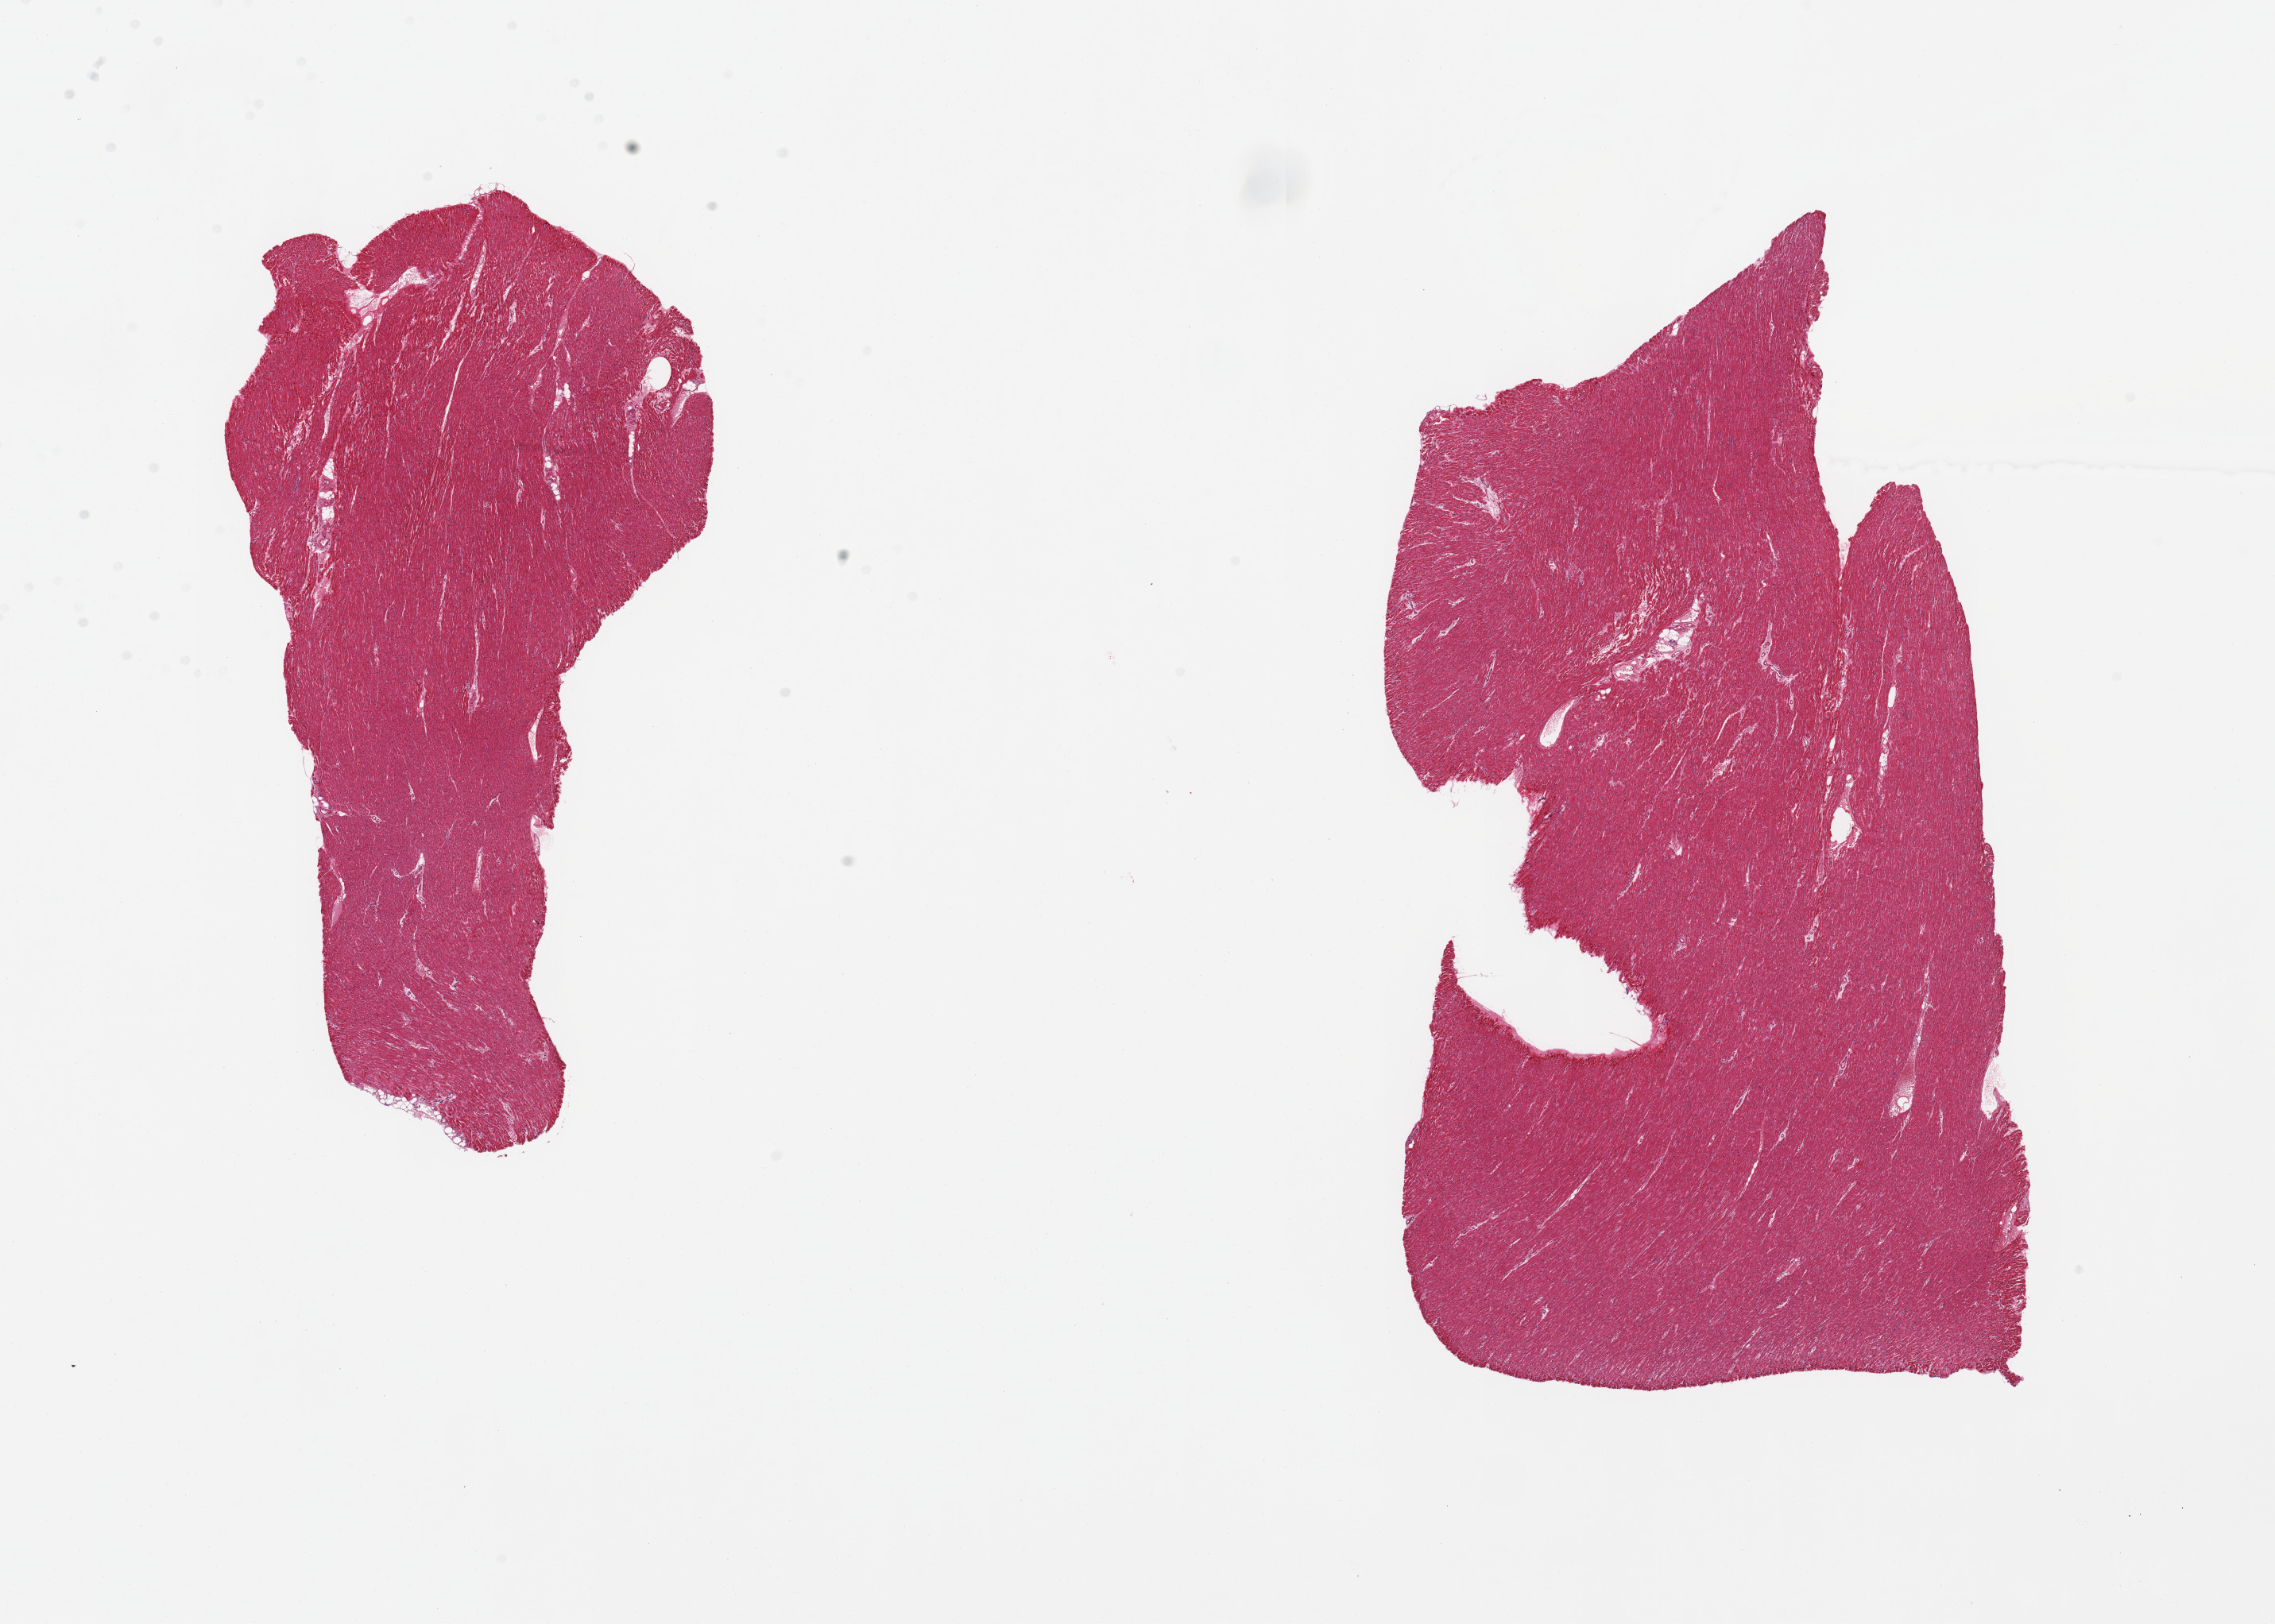
Whole-slide image, H&E stain, brightfield — shown as a low-resolution overview of the whole scanned area (about 22.6 x 16.2 mm, slide scanned at 20x), PAXgene-fixed paraffin-embedded (PFPE) section, target tissue: heart, donor tissue sample. Female donor.
- pathologist's review note for this sample: 2 pieces, mild interstitial fibrosis/ chronic ischemic changes